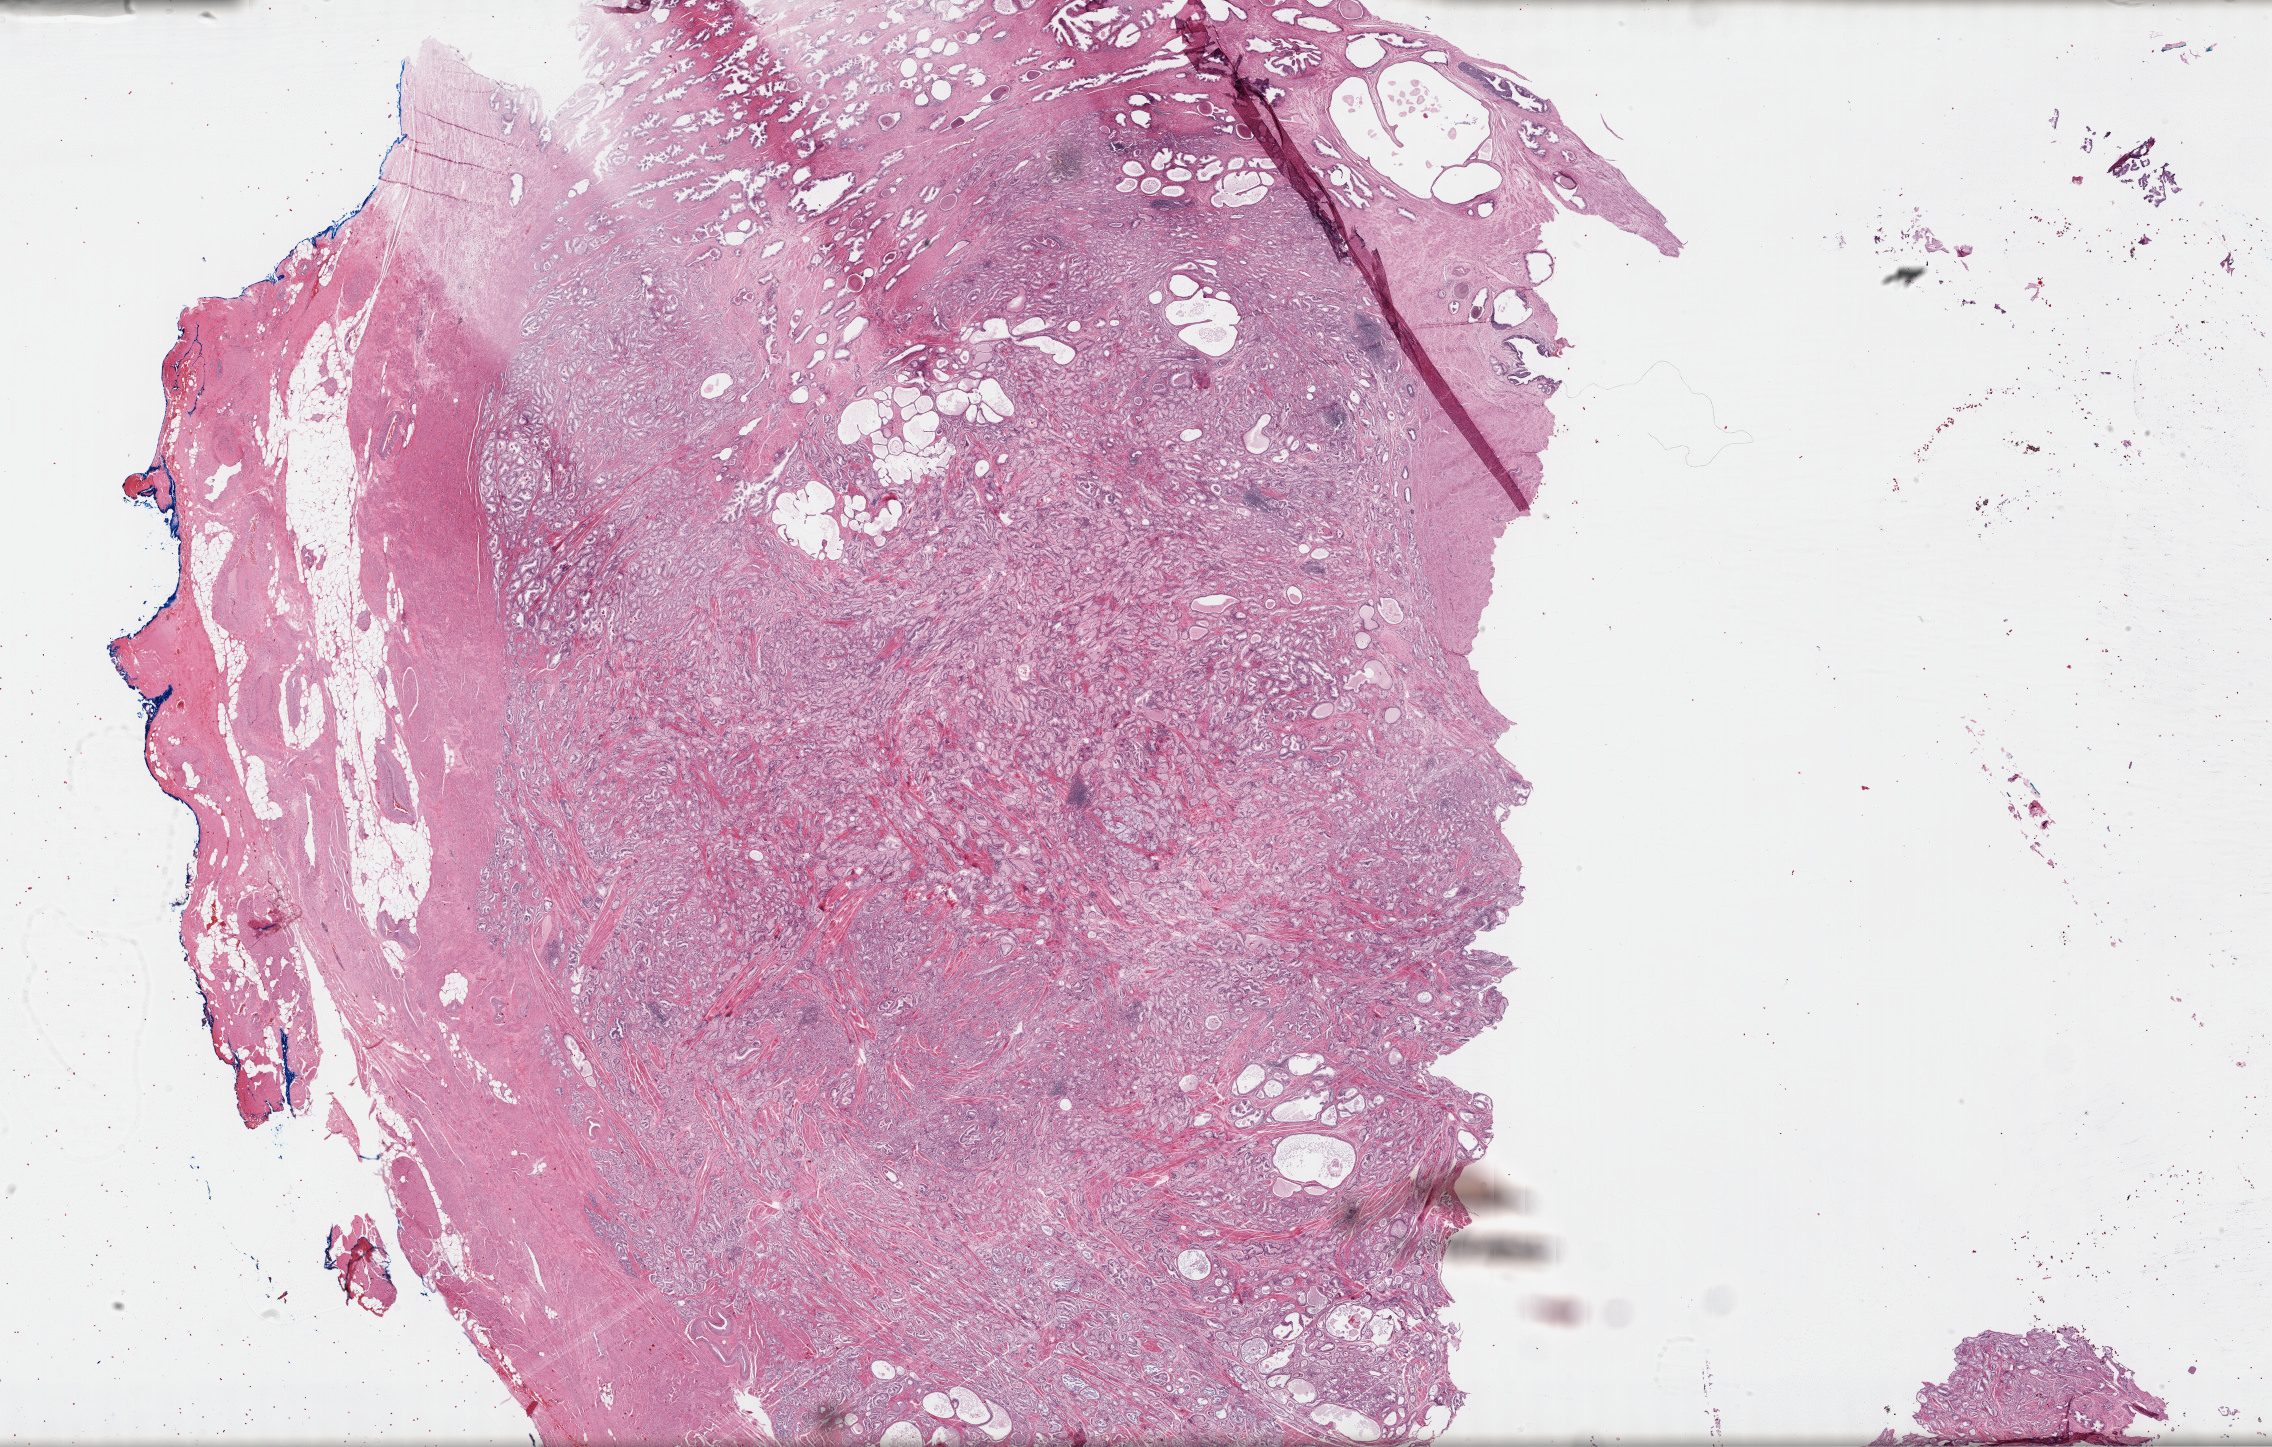
Whole-slide histology image, H&E-stained, whole scanned area (about 36.7 x 23.4 mm, from a 40x scan) shown as a low-resolution overview. FFPE section. Primary tumour sample from the prostate. Patient: male, age at initial diagnosis 57 years. Gleason score: 6 (3+3).
Diagnosis: Adenocarcinoma, NOS. Laterality: bilateral.